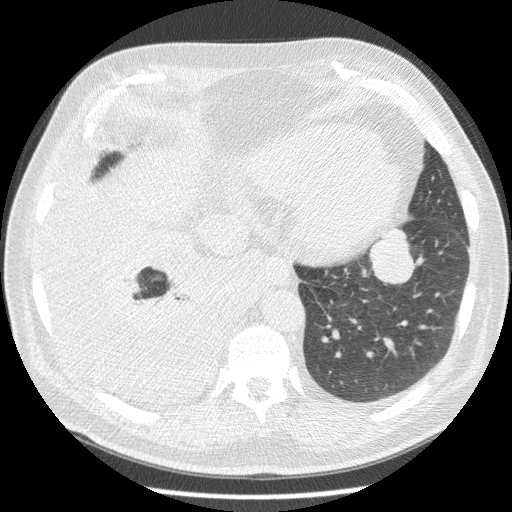
Low-dose screening chest CT, axial slice; third annual screen; lung window (W 1500 / L -600 HU); 2.5 mm slice thickness; standard (soft-tissue) reconstruction kernel (STANDARD); 120 kVp; slice 57 of 180 in the series. Male, age 63 years at enrolment. Current smoker at enrolment.
Expert reader's lesion annotation, box from (x=354, y=221) to (x=419, y=289) px. Screening reader's record for this exam (one nodule recorded; not confirmed to be the boxed lesion): non-calcified nodule or mass ≥4 mm, left lower lobe, 34 × 31 mm, smooth margins, soft tissue attenuation, pre-existing on the prior screen: yes; interval growth: yes. Official screen result: positive, other. Lung cancer was diagnosed 30 days after this screen: squamous cell carcinoma, NOS, left lower lobe, stage IB (AJCC 6th edition), 48 mm at pathology.